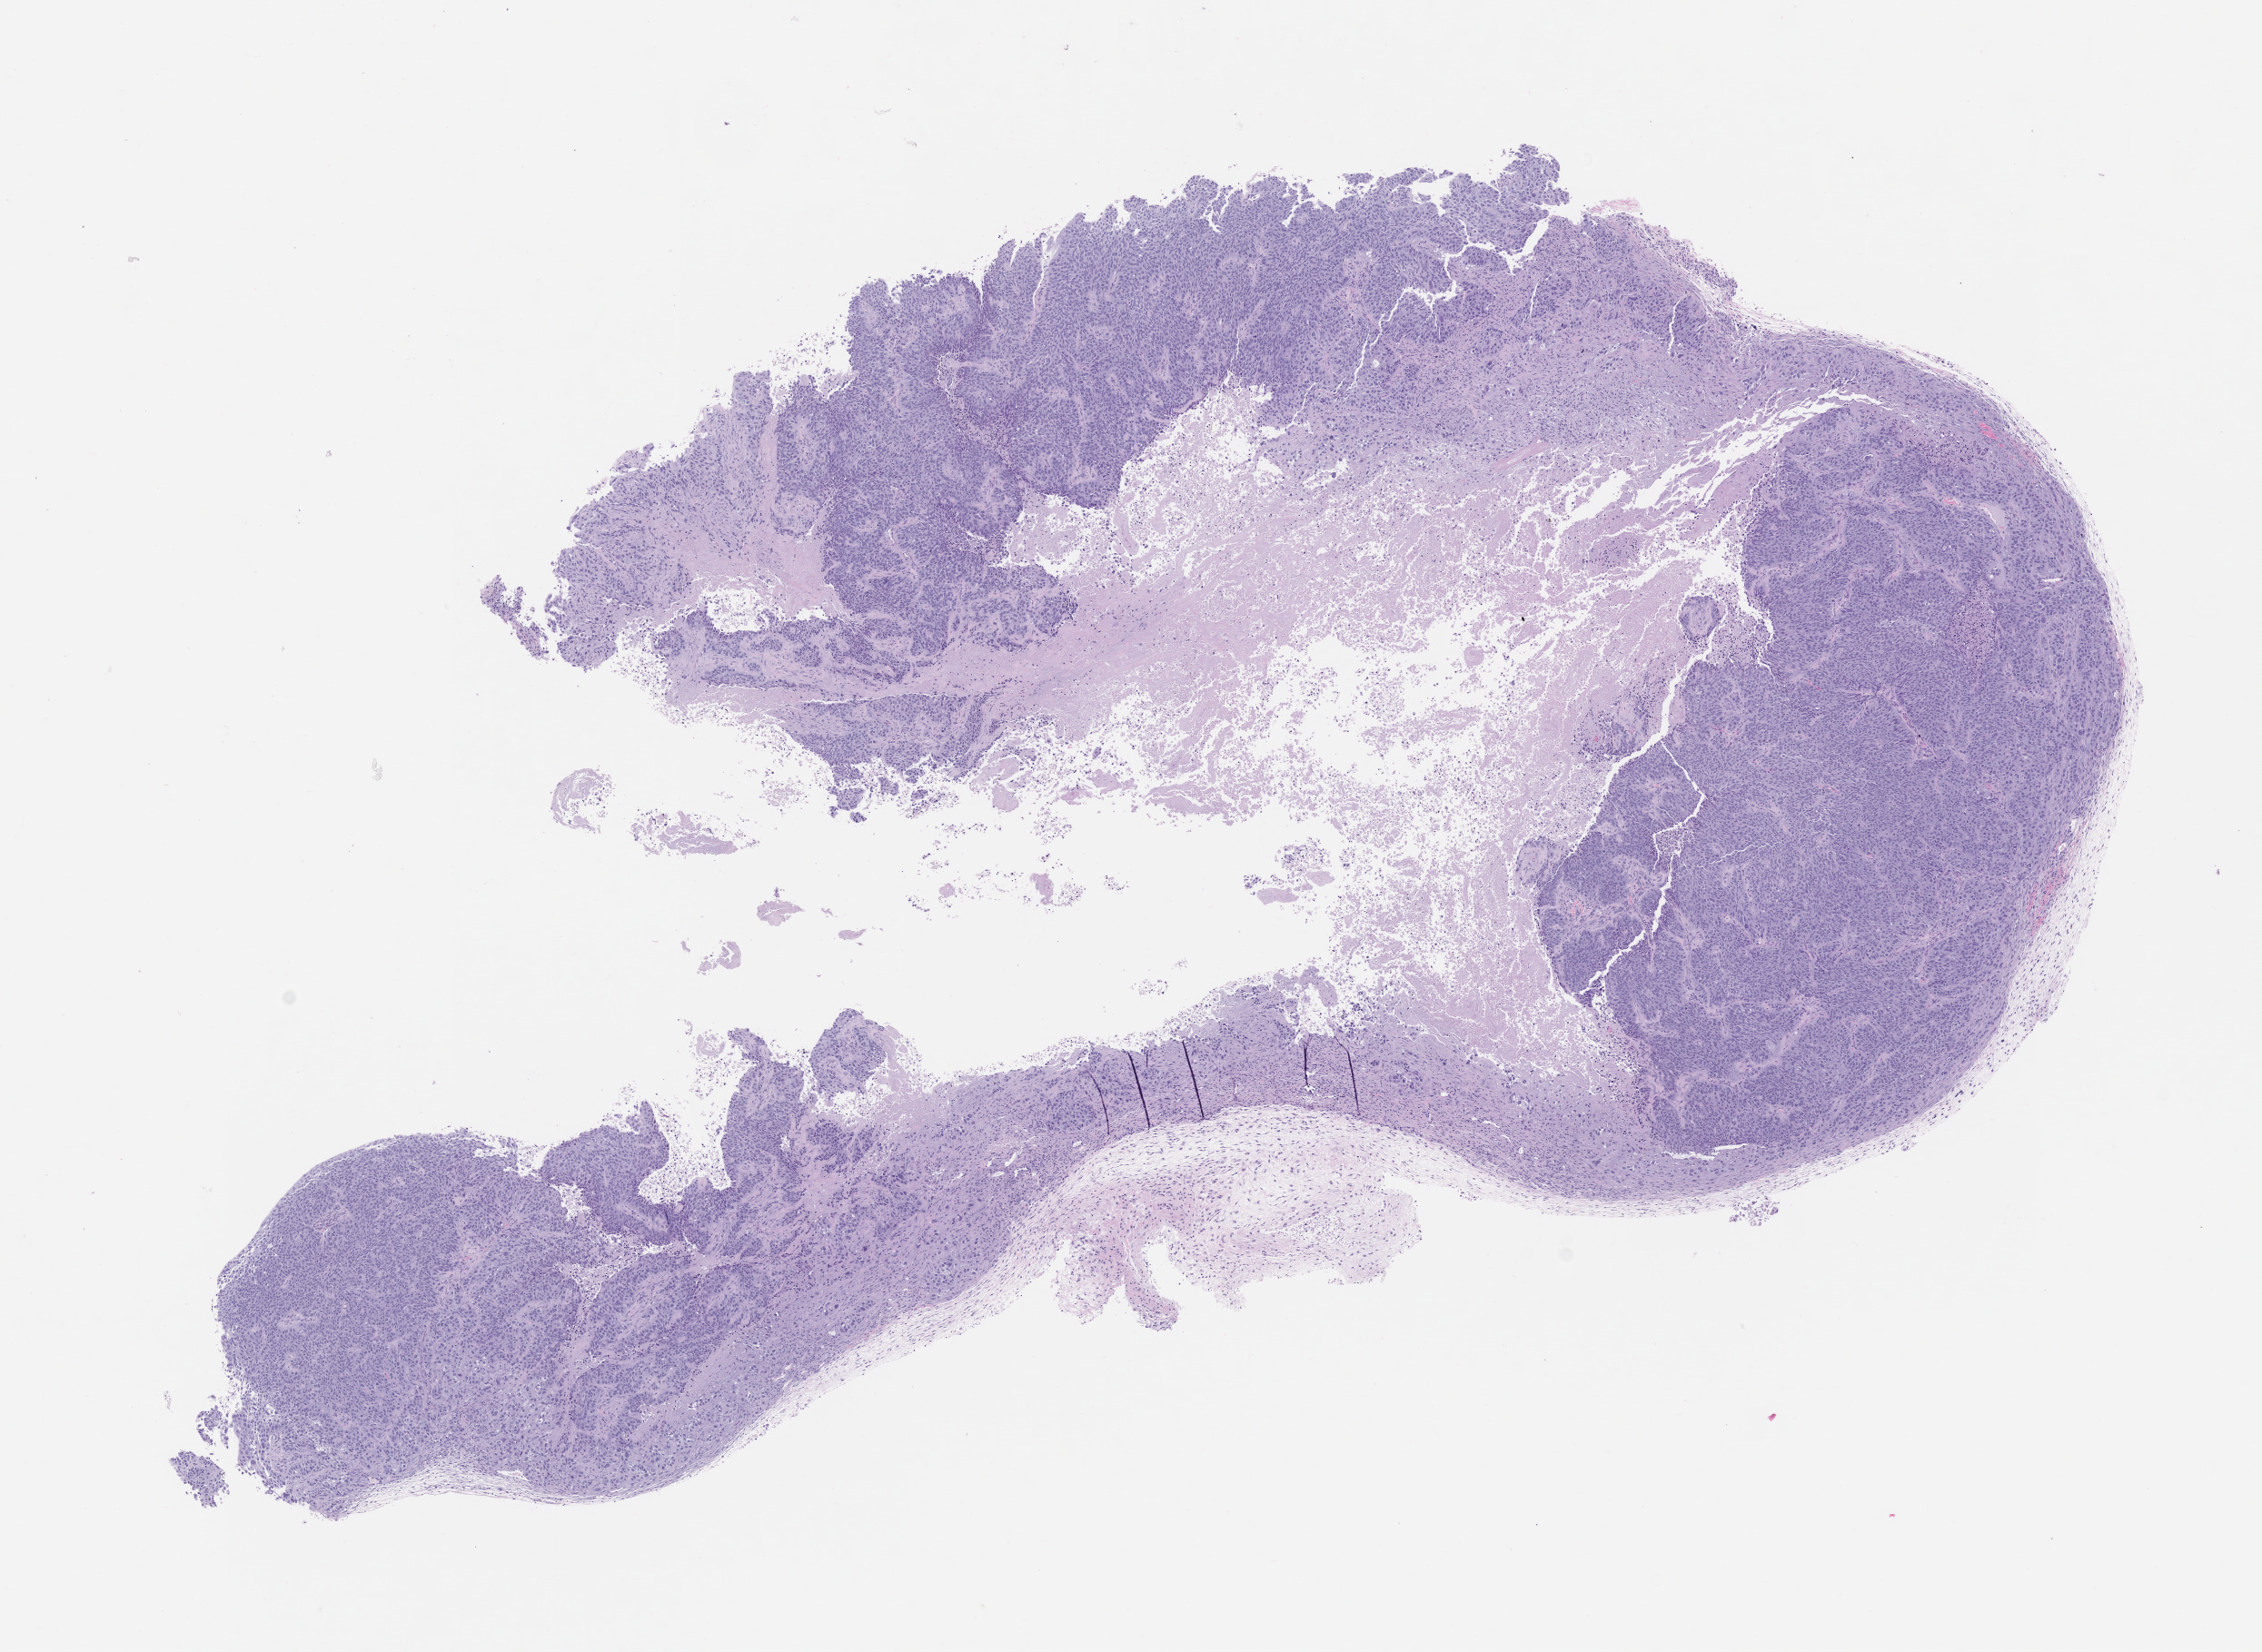
Whole-slide image, haematoxylin and eosin: patient-derived xenograft (human tumor grown in a mouse), passage 0 — shown as a low-resolution overview of the whole scanned area (about 10.0 x 7.3 mm). FFPE section. Originating tumor site category: lung.
Originating patient diagnosis: Lung Squamous Cell Carcinoma.